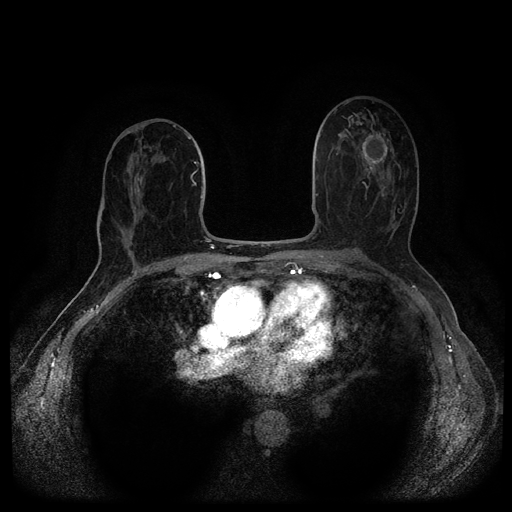
Breast MRI (dynamic contrast-enhanced, multi-phase), one axial slice. Position 55 of 116 along the scan axis. Dynamic contrast-enhanced series, time point 2 of 5 at this slice position (early post-contrast). 1.5 T. TE 2.6 ms, TR 5.4 ms. 512 × 512 image matrix, field of view 340 × 340 mm. Female patient, age 69 years.
Outlined on this slice (semi-automatic segmentation, software-assisted and operator-edited):
- breast lesion (labelled benign in the annotation): bounding box [x1, y1, x2, y2] px = [358, 130, 391, 176]